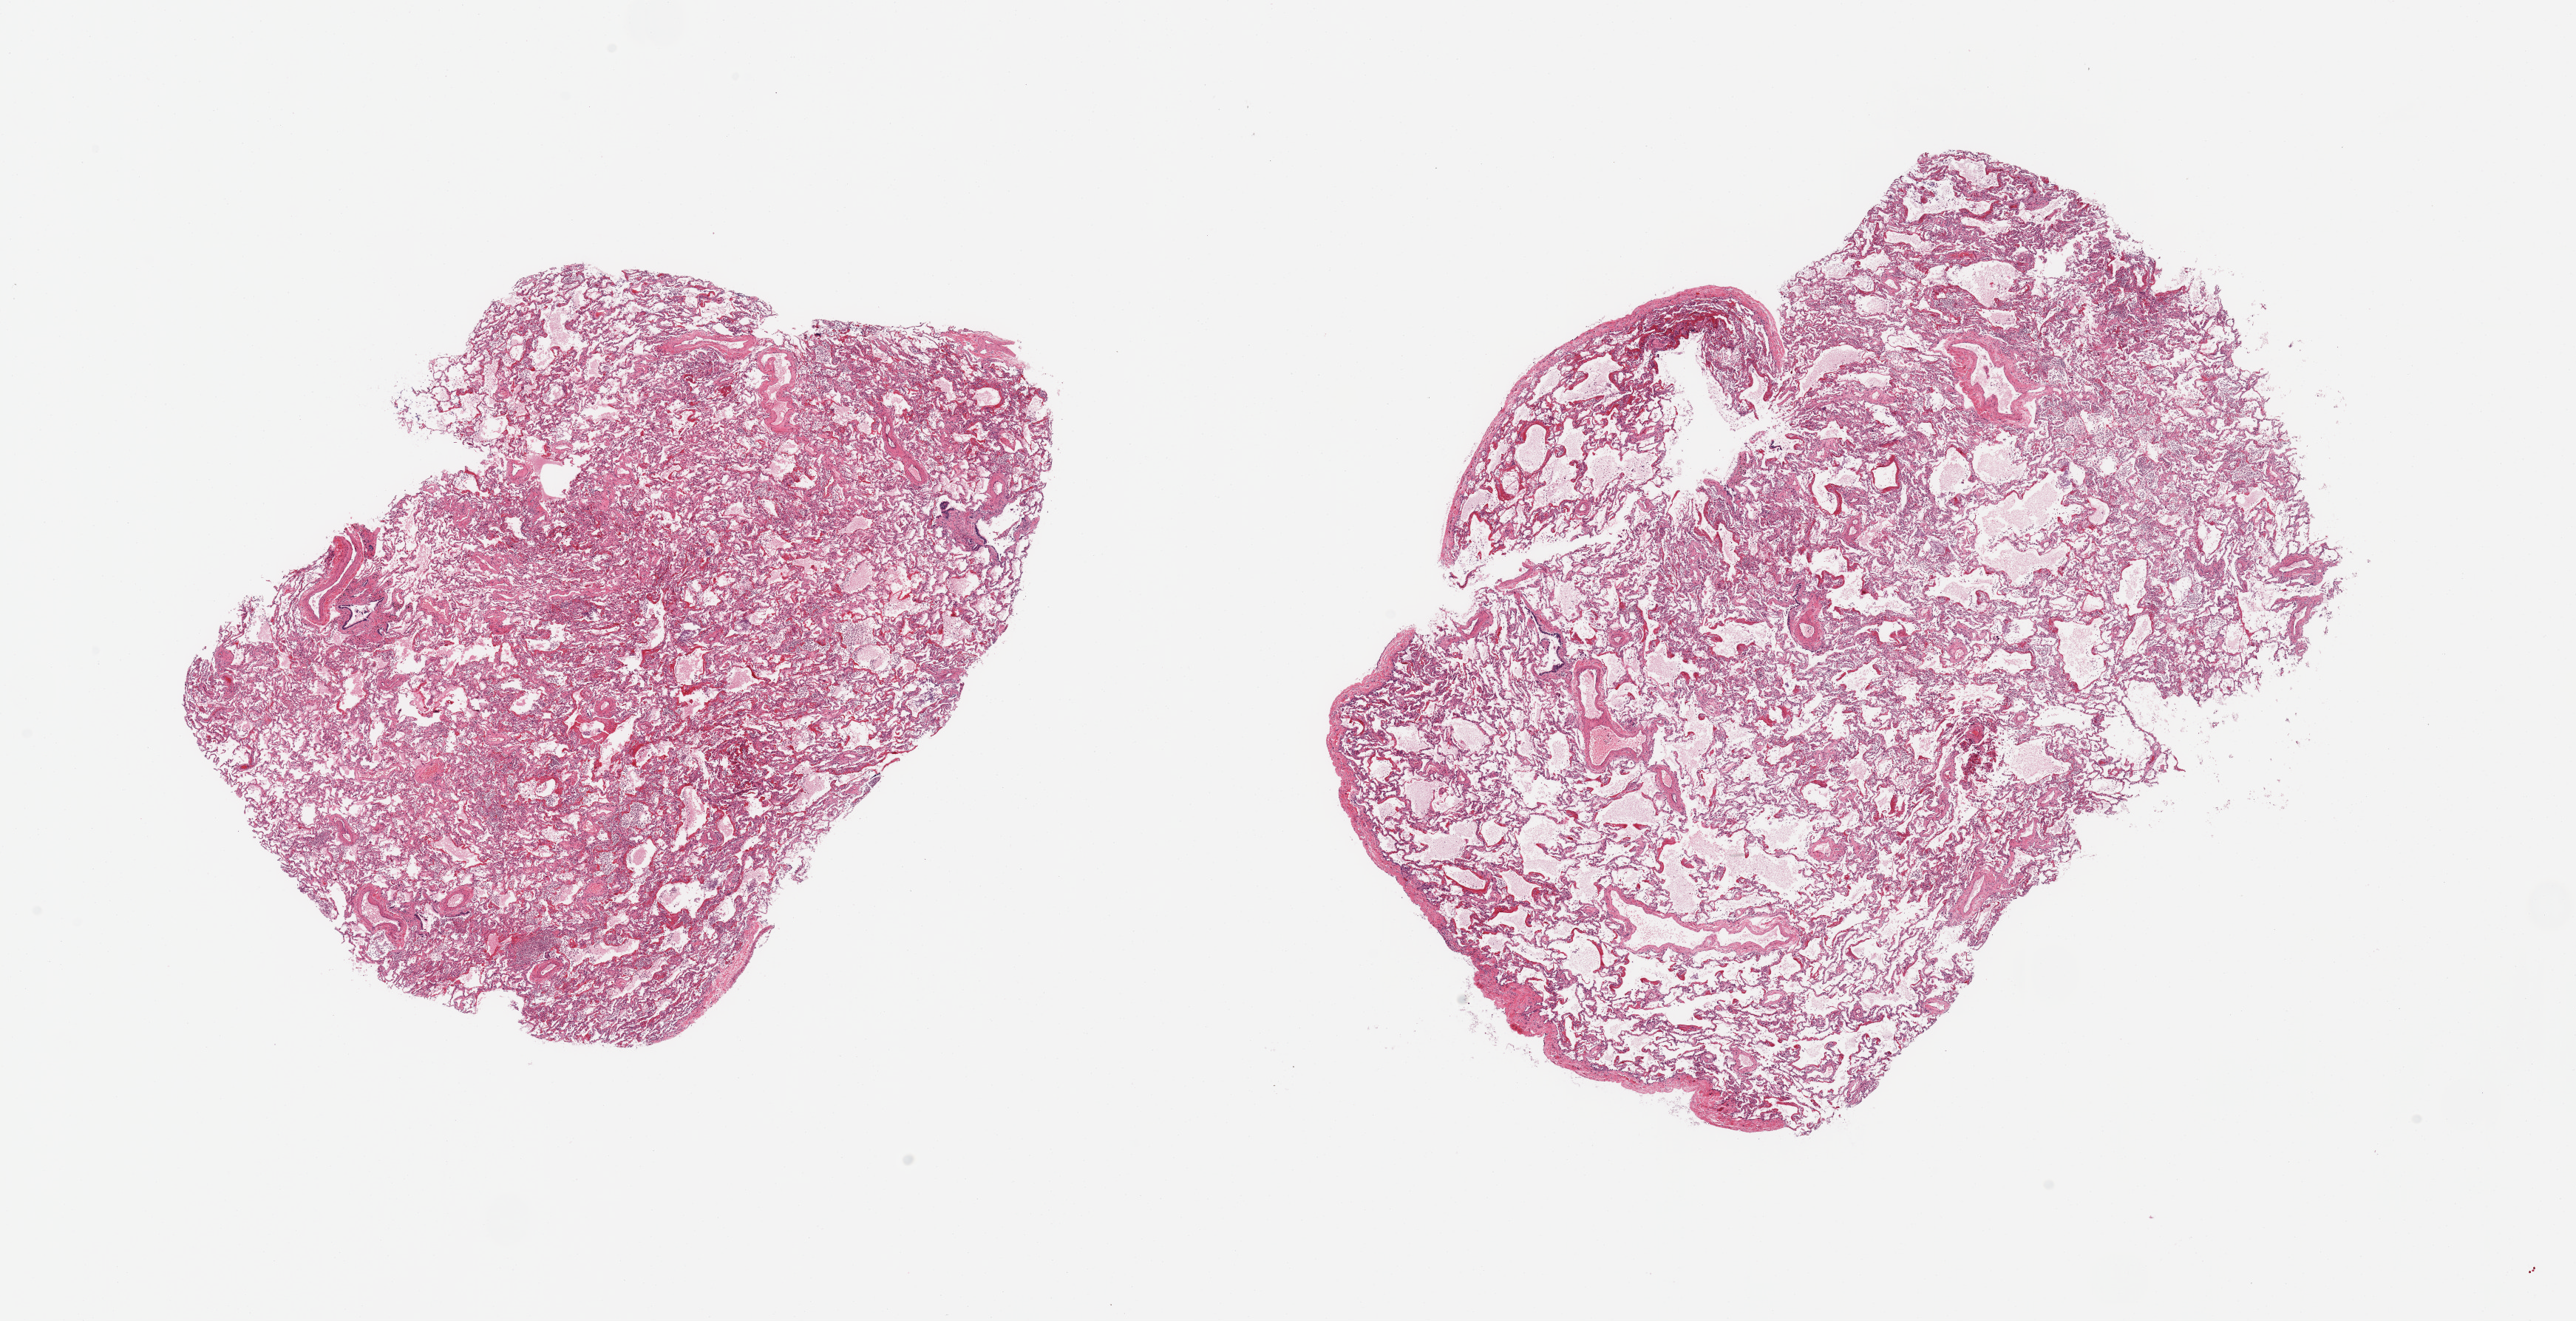
Digitized H&E-stained section, shown as a low-resolution overview of the whole scanned area (about 27.6 x 14.1 mm, slide scanned at 20x), PAXgene-fixed paraffin-embedded (PFPE) section, target tissue: lung, tissue donor sample. Female donor.
Review note (as recorded): 2 pieces; 1 piece include pleura (target is 1cm below pleura), diffuse pneumonia and fibrin deposition, edema.